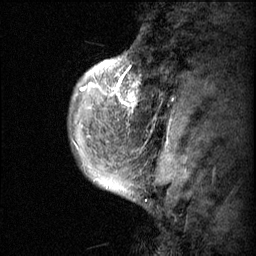
Breast MRI (dynamic contrast-enhanced), one sagittal slice. Dynamic contrast-enhanced series, image 2 of 3 at this slice position (ordered by acquisition). 1.5 T. TE 4.2 ms, TR 11.1 ms. 2 mm slice thickness. 256 × 256 image matrix, field of view 180 × 180 mm. Female patient, age 50 years.
Outlined on this slice (semi-automatic segmentation, software-assisted and operator-edited):
- analysis volume of interest (the breast-tissue region the enhancement analysis was run in; not a lesion): bounding box [x1, y1, x2, y2] px = [82, 56, 154, 143]
- tumour enhancement mask (voxels above the 70 % enhancement threshold inside the analysis volume of interest): [82, 56, 141, 139]